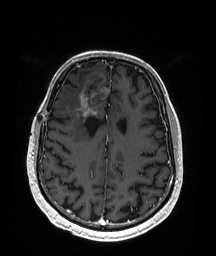
Brain MRI from a brain-tumour surgery series, one axial slice; position 67 of 192 along the scan axis; T1-weighted post-contrast; 1 mm slice thickness; 216 × 256 image matrix, field of view 211 × 250 mm. From the clinical record (not read from this slice): histopathology: Astrocytoma; WHO grade: 3; IDH mutation: yes; tumour location: Right Frontal.
Structures marked on this image (expert manual segmentation):
- previous resection cavity: box from (x=81, y=83) to (x=96, y=120) px
- tumour: (x=79, y=90)–(x=97, y=118)